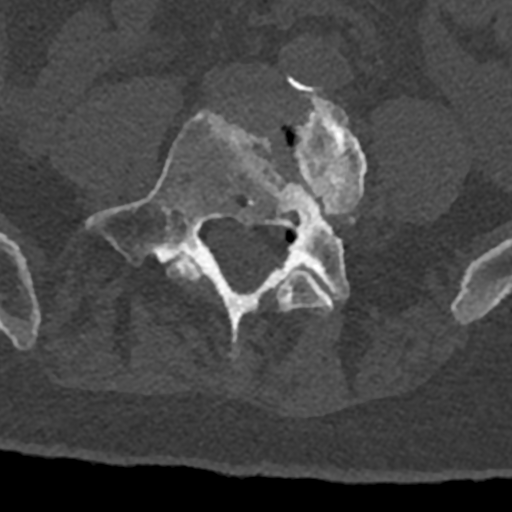
CT including the spine, one axial slice; slice 219 of 797 in the series (ordered by position); reconstruction kernel Br40s/3; 120 kVp; bone window (W 1800 / L 400 HU); 0.5 mm slice thickness; 512 × 512 image matrix. Male patient, age 74 years. Case-level facts recorded for this patient, not image findings: primary cancer: renal; vertebrae with lytic lesions (as recorded): T10, L1, L2, L3, L4, L5.
Outlined on this slice (semi-automatically segmented with operator editing):
- L4 vertebra: bounding box [x1, y1, x2, y2] px = [167, 81, 367, 315]
- L5 vertebra: [85, 111, 349, 358]